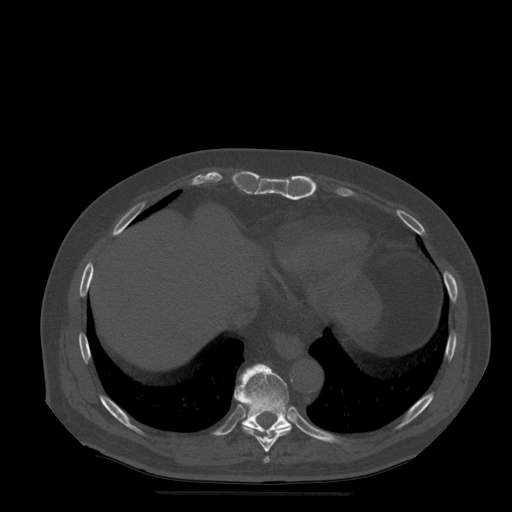
CT including the spine, one axial slice; slice 279 of 522 in the series (ordered by position); bone window (W 1800 / L 400 HU); 512 × 512 image matrix, field of view 420 × 420 mm. Patient age 72 years. From the clinical record (not read from this slice): primary cancer: prostate.
Annotated regions visible in this slice (semi-automatic segmentation, software-assisted and operator-edited):
- T10 vertebra: bounding box (x1, y1, x2, y2) in pixels: (235, 364, 291, 434)
- T8 vertebra: (264, 457, 270, 464)
- T9 vertebra: (235, 392, 292, 452)